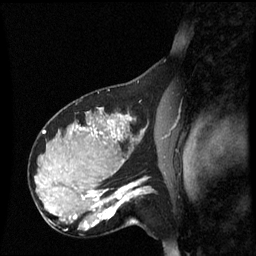
Breast MRI (dynamic contrast-enhanced), one sagittal slice; slice 37 of 60 in the series (ordered by position); dynamic contrast-enhanced series, image 2 of 3 at this slice position (ordered by acquisition); 1.5 T; TE 4.2 ms, TR 8.9 ms; 2.2 mm slice thickness; 256 × 256 image matrix, field of view 220 × 220 mm. Female patient, age 31 years. Case-level facts recorded for this patient, not image findings: setting: breast cancer imaged before/during neoadjuvant chemotherapy; receptor status: HR-positive, HER2-negative.
Annotated regions visible in this slice (semi-automatic segmentation, software-assisted and operator-edited):
- analysis volume of interest (the breast-tissue region the enhancement analysis was run in; not a lesion): bounding box [x1, y1, x2, y2] px = [90, 180, 152, 229]
- tumour enhancement mask (voxels above the 70 % enhancement threshold inside the analysis volume of interest): [90, 180, 143, 227]